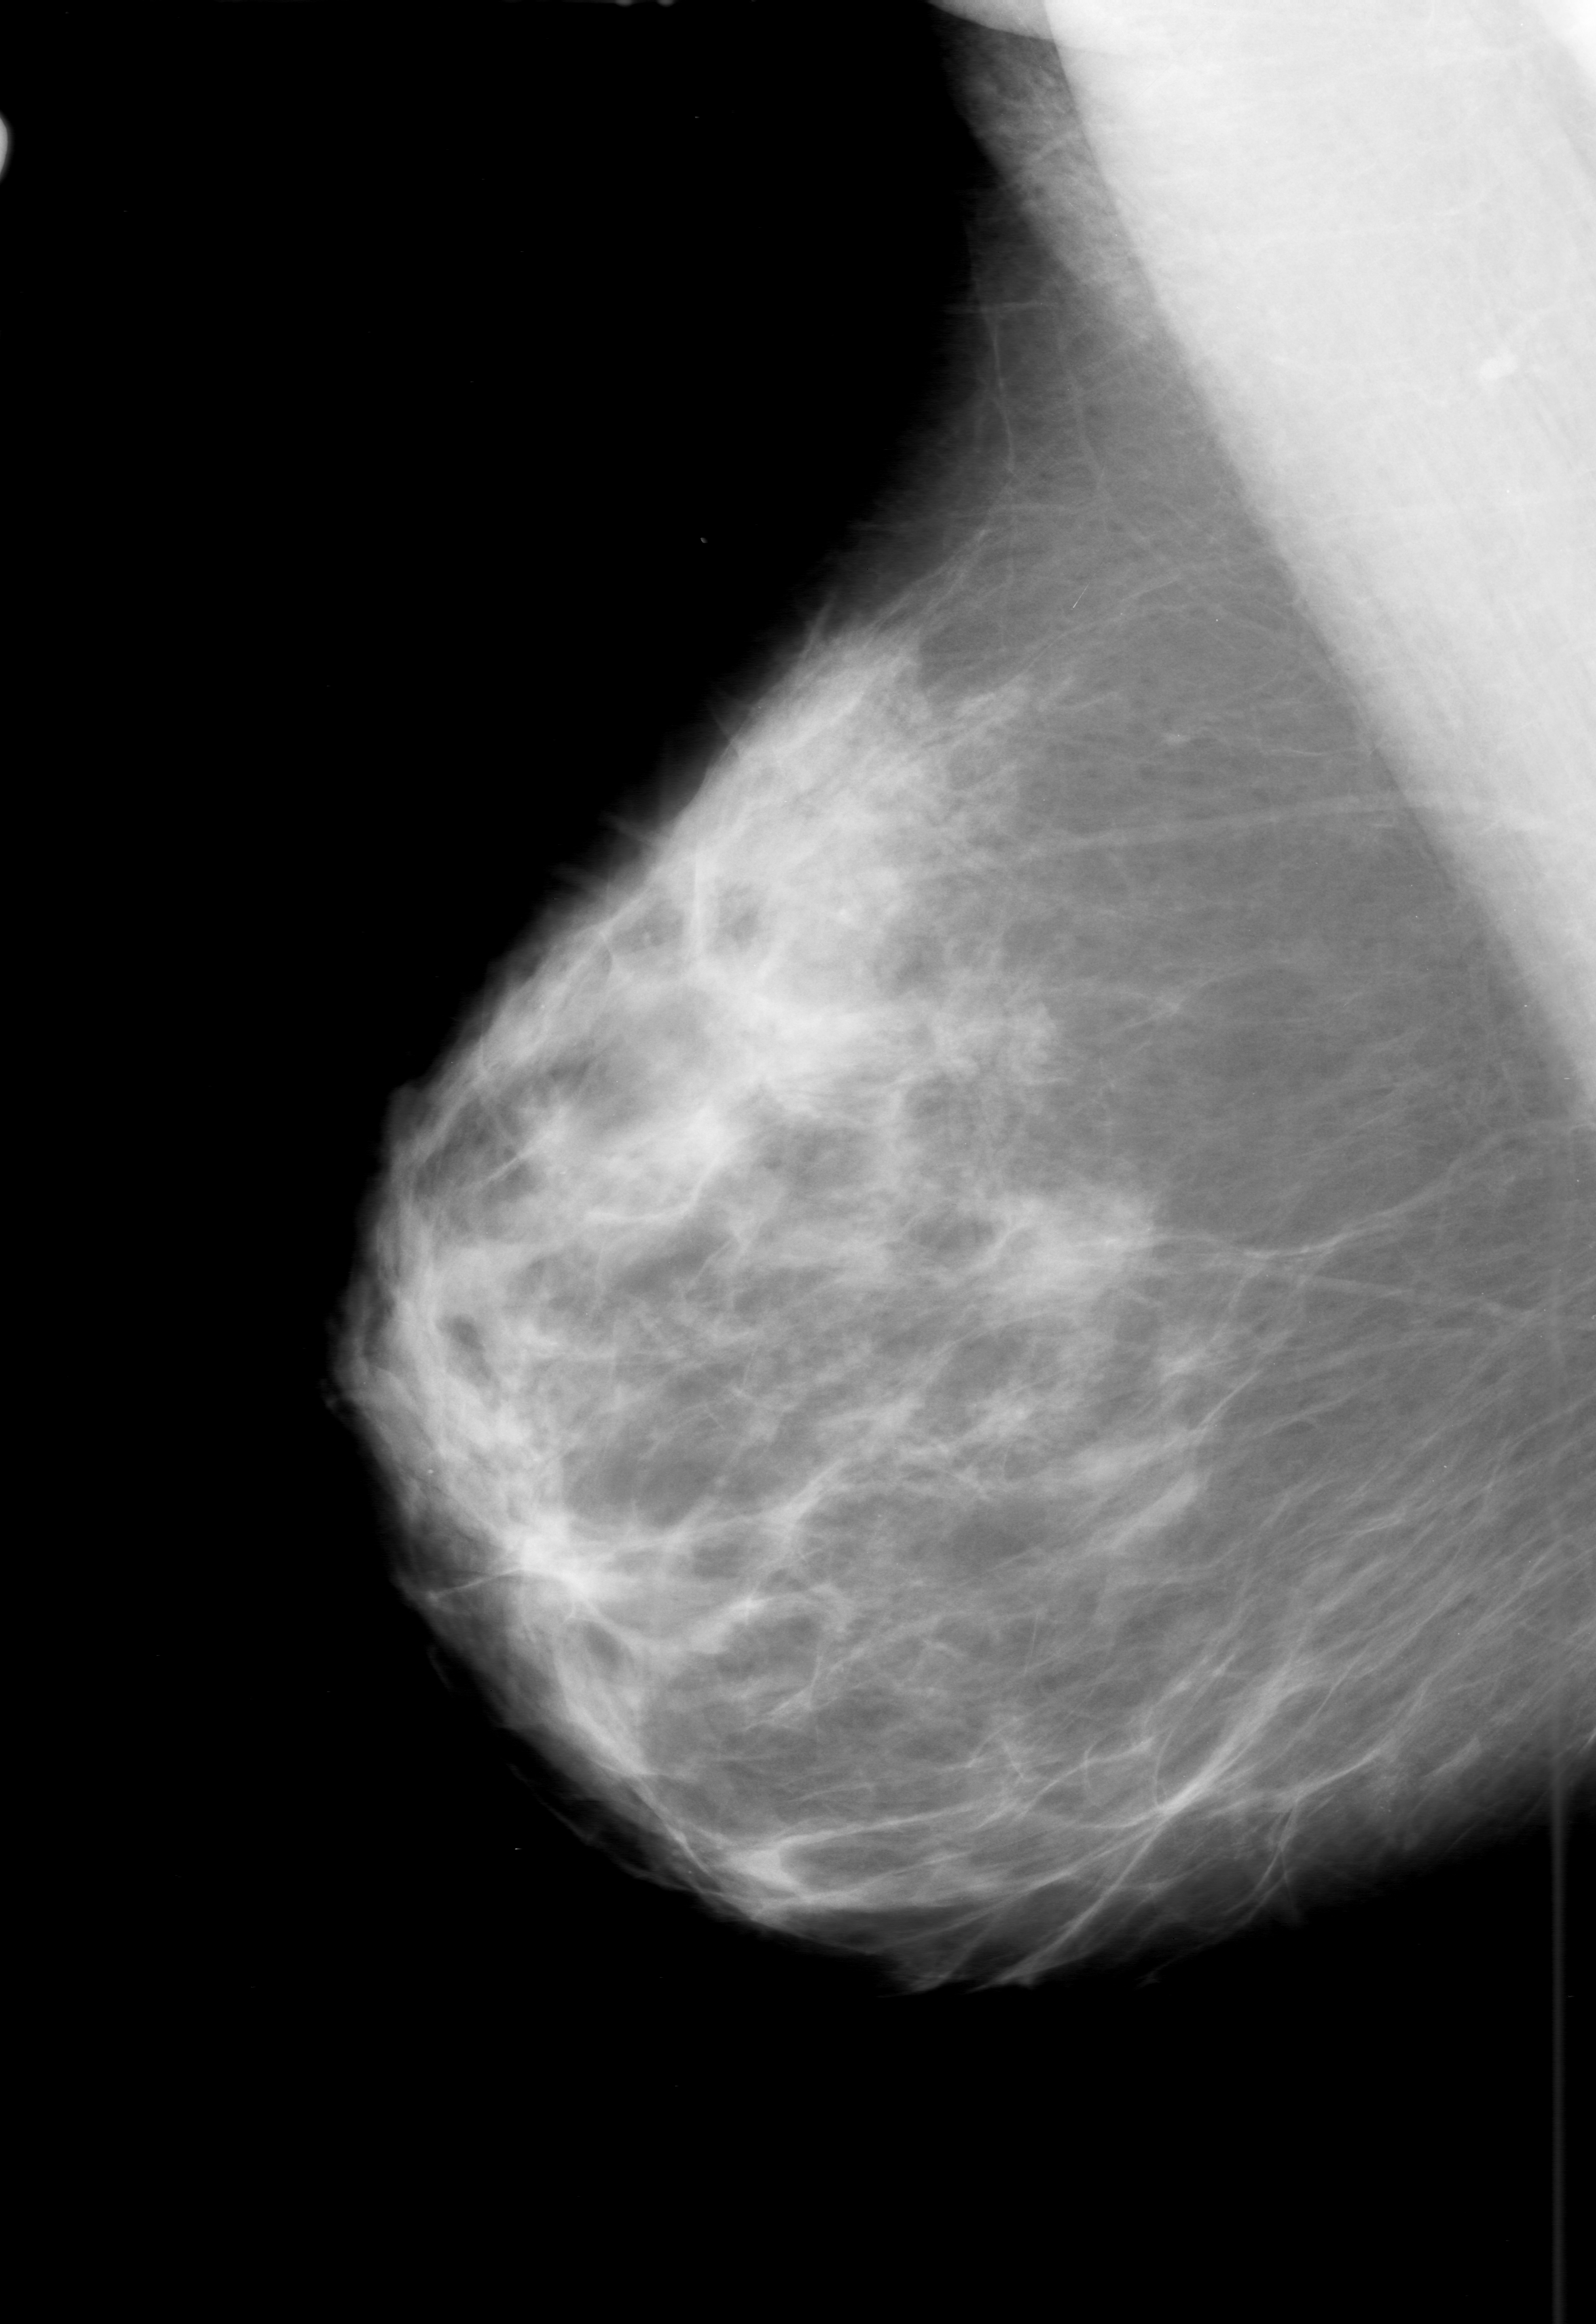
Mammogram (digitized film), right breast, mediolateral oblique (MLO) view, breast composition: scattered fibroglandular densities (BI-RADS density category 2 of 4).
Marked findings (only marked abnormalities are described; nothing is implied about the rest of the image): calcifications, morphology punctate, distribution clustered; BI-RADS assessment category 0 (incomplete: needs additional imaging); pathology result (as recorded, not read from the image): benign.